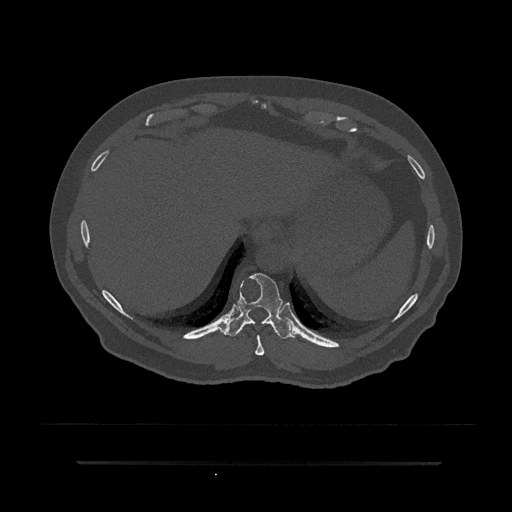
CT including the spine, one axial slice; slice 339 of 797 in the series (ordered by position); reconstruction kernel Br40s/3; 120 kVp; bone window (W 1800 / L 400 HU); 512 × 512 image matrix. Male patient, age 59 years. Case-level facts recorded for this patient, not image findings: primary cancer: bile ducts; vertebrae with lytic lesions (as recorded): T10.
Structures marked on this image (semi-automatically segmented with operator editing):
- T10 vertebra: bounding box (x1, y1, x2, y2) in pixels: (225, 273, 295, 339)
- T9 vertebra: (255, 335, 265, 356)